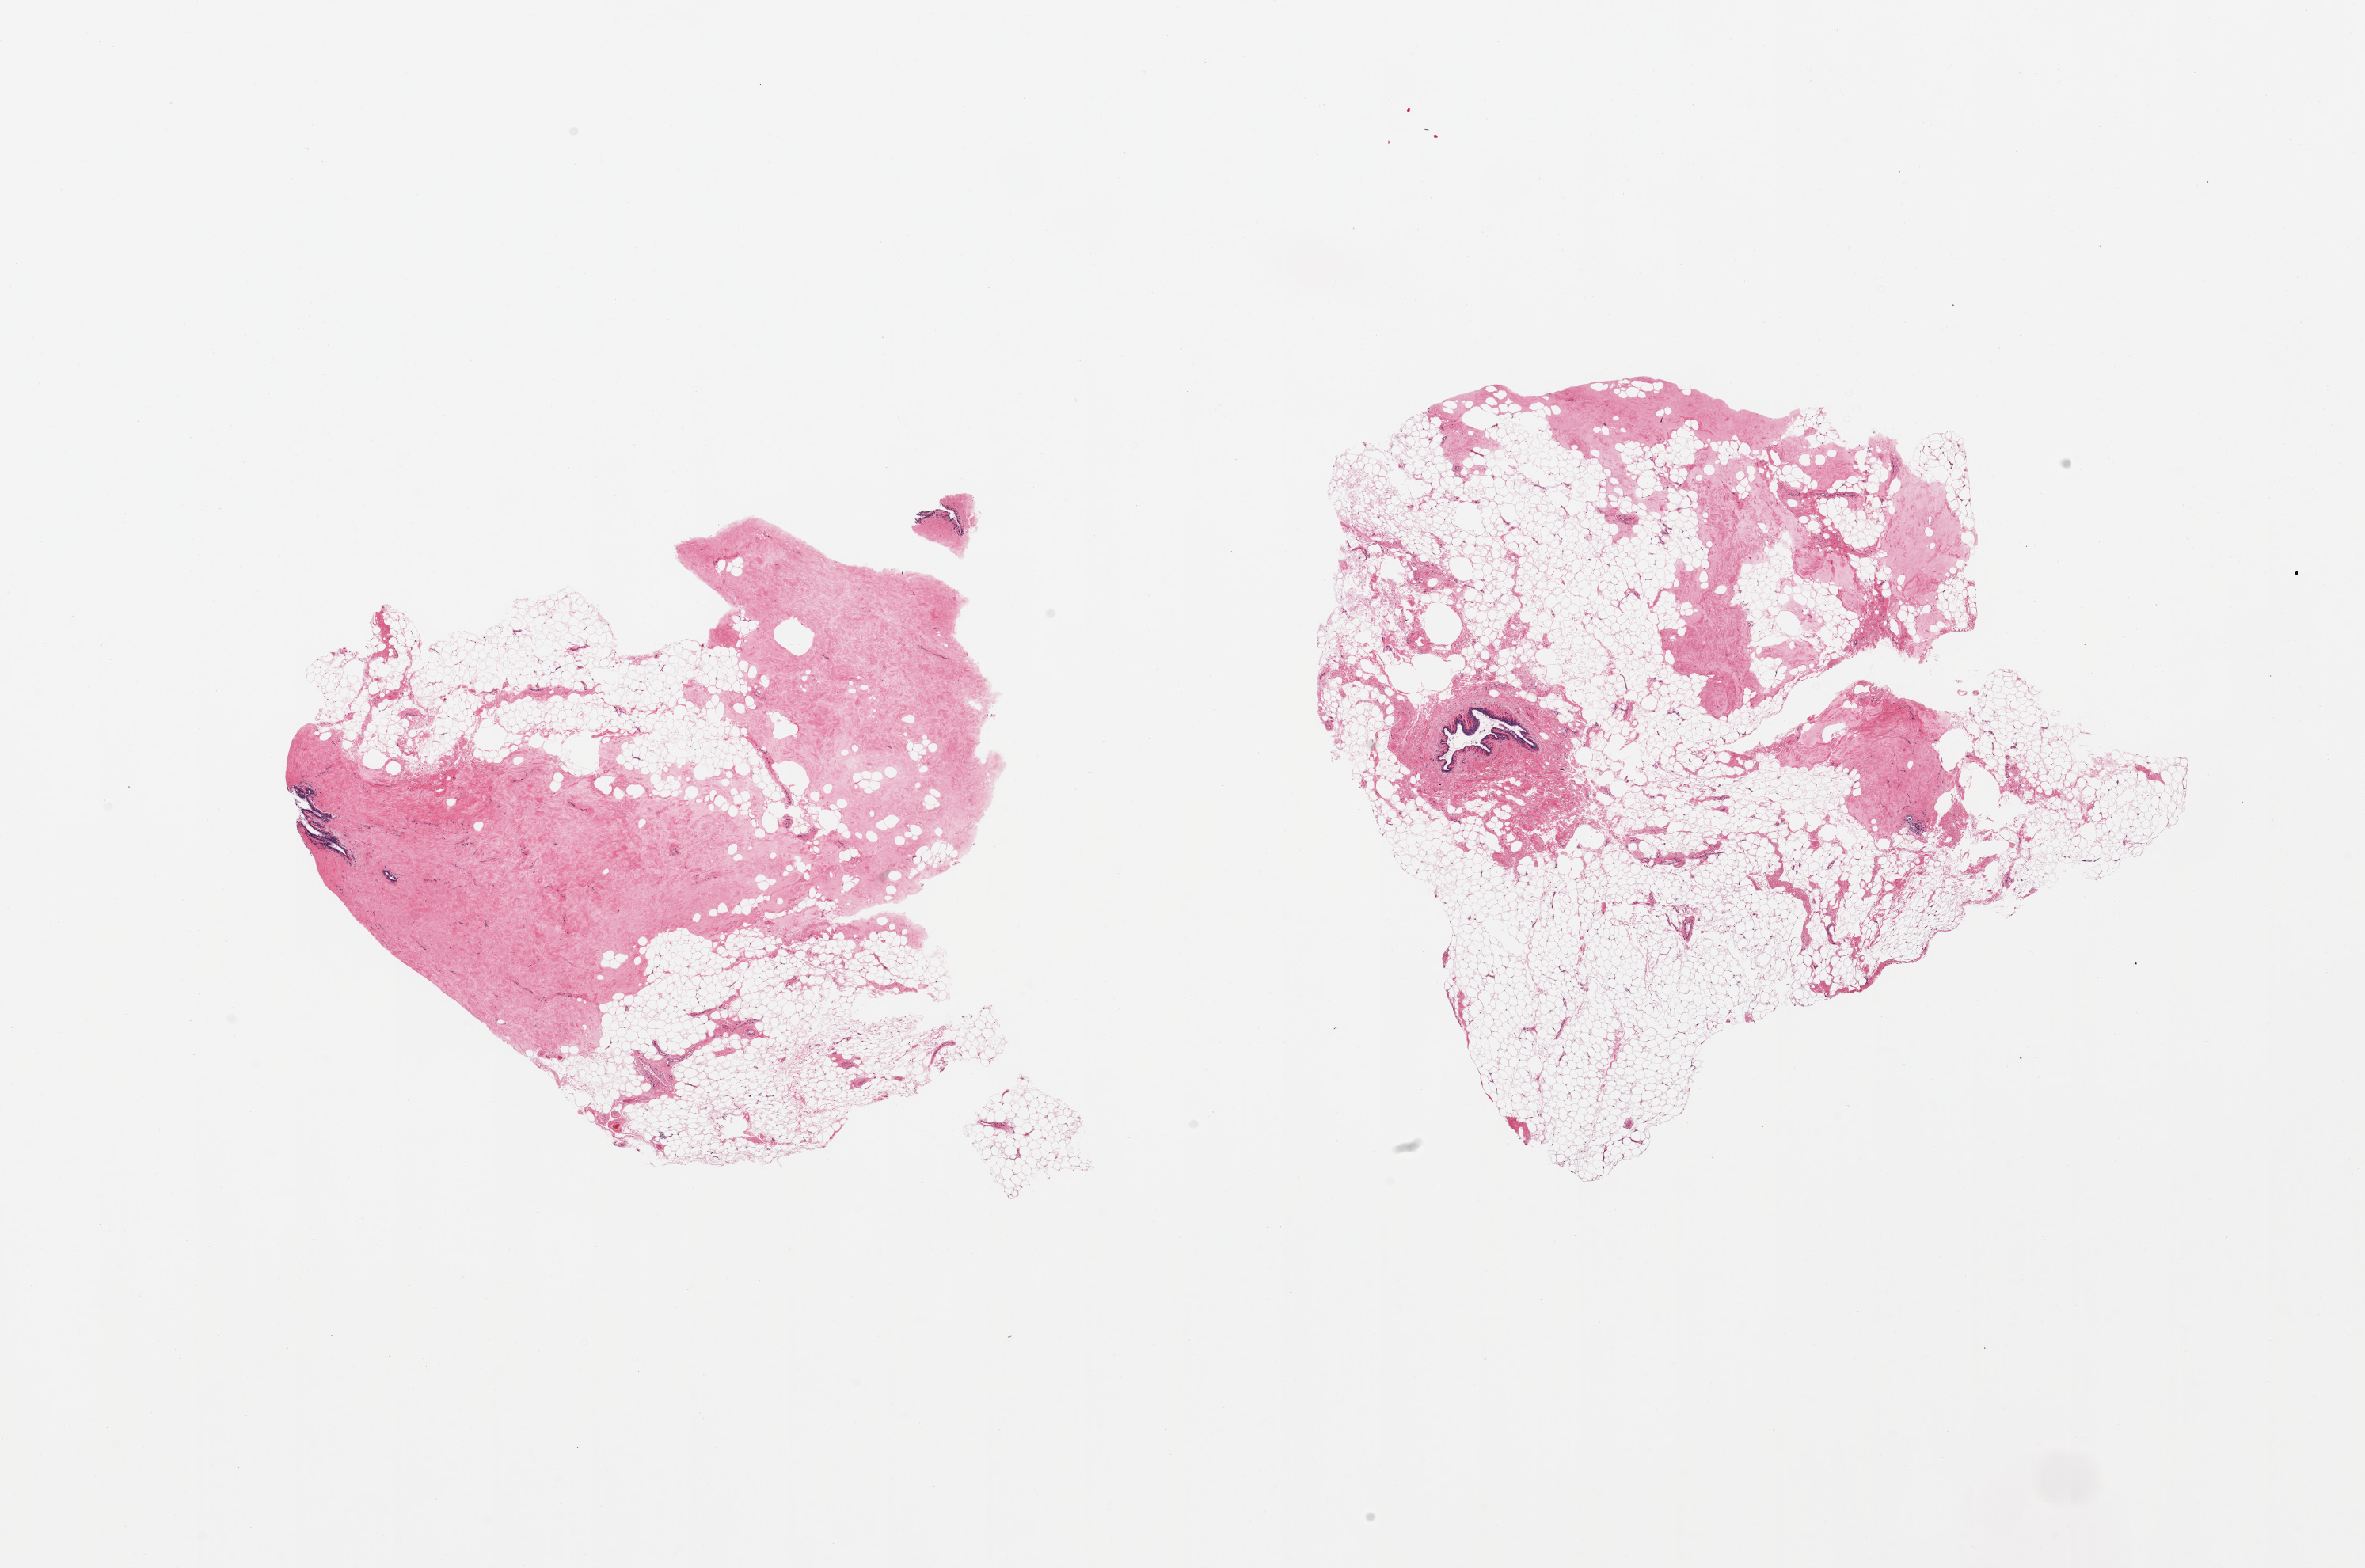
Digitized haematoxylin and eosin-stained section, low-resolution overview of the scanned area, about 23.6 x 15.7 mm, PAXgene-fixed paraffin-embedded (PFPE) section, target tissue: breast, tissue donor sample. Female donor.
Pathologist's review note for this sample: 2 pieces; atrophic ducts (no lobules) in fibroadipose tissue.